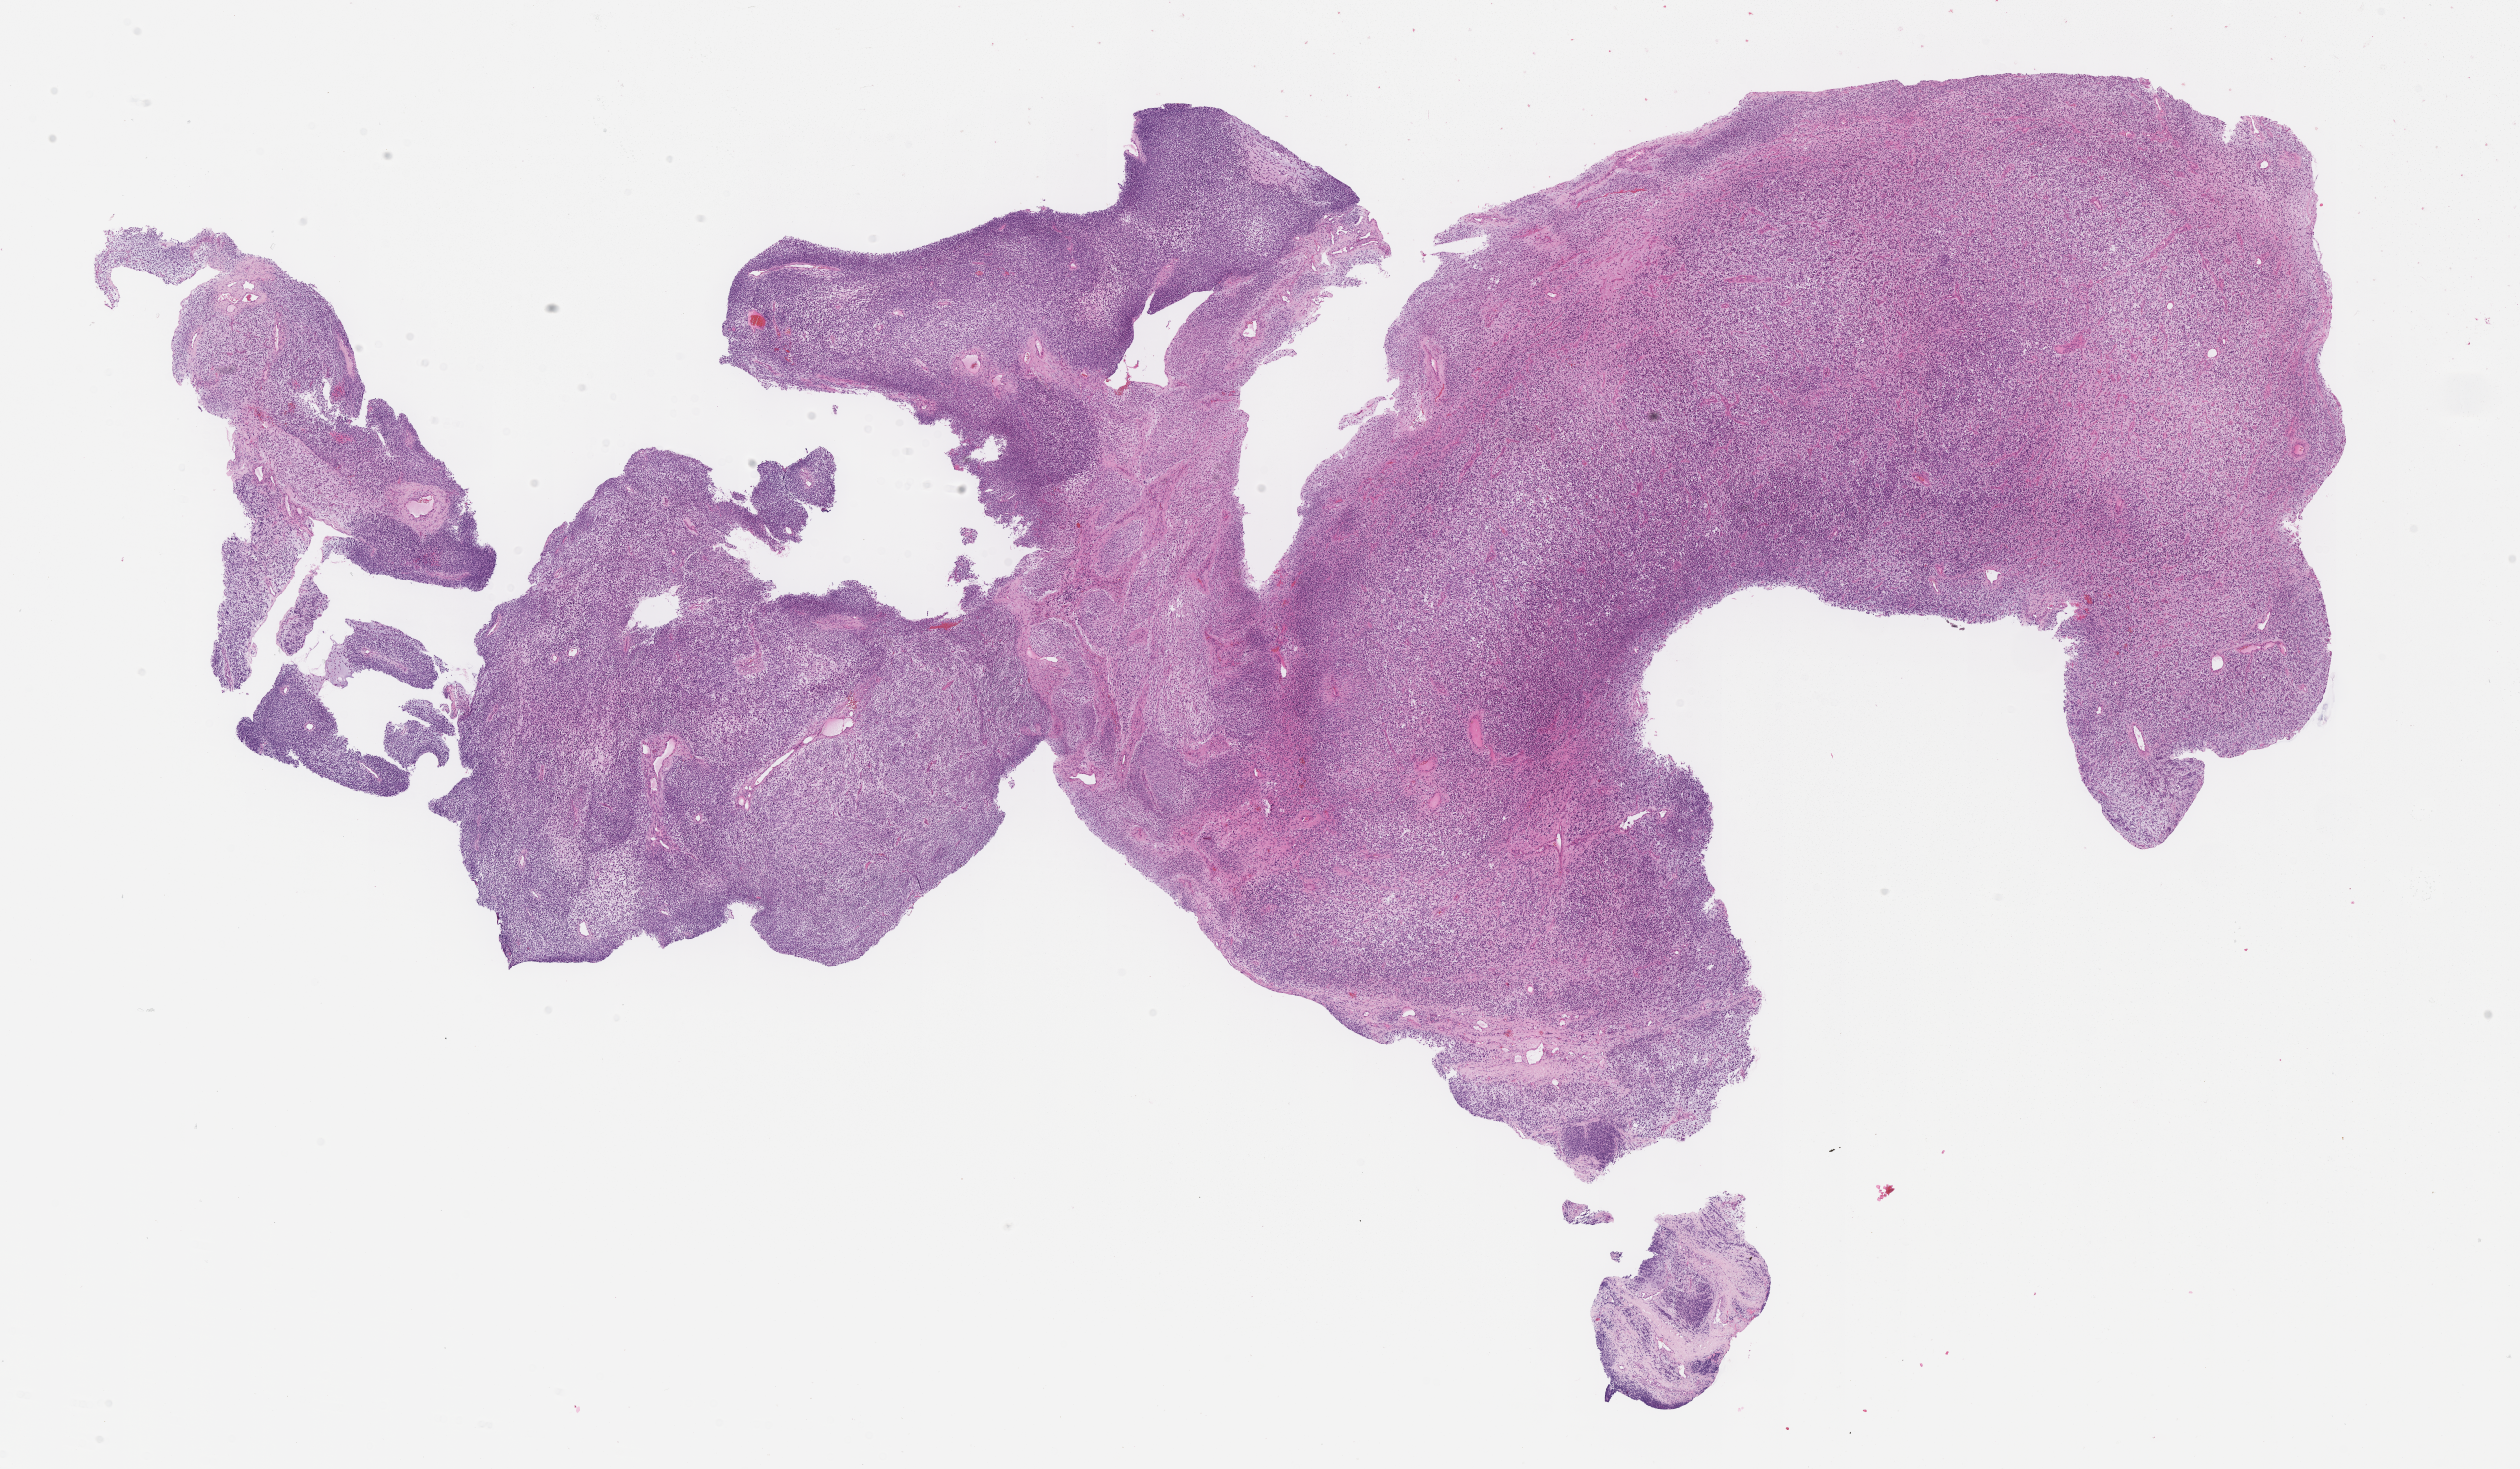
Digitized H&E-stained section of tumor tissue, low-resolution overview of the scanned area, about 20.6 x 12.0 mm, formalin-fixed, paraffin-embedded (FFPE) tissue, site: soft tissue, pelvis-left. Male patient, age at diagnosis 4.3 years.
Diagnosis: rhabdomyosarcoma; histological classification: embryonal rhabdomyosarcoma.